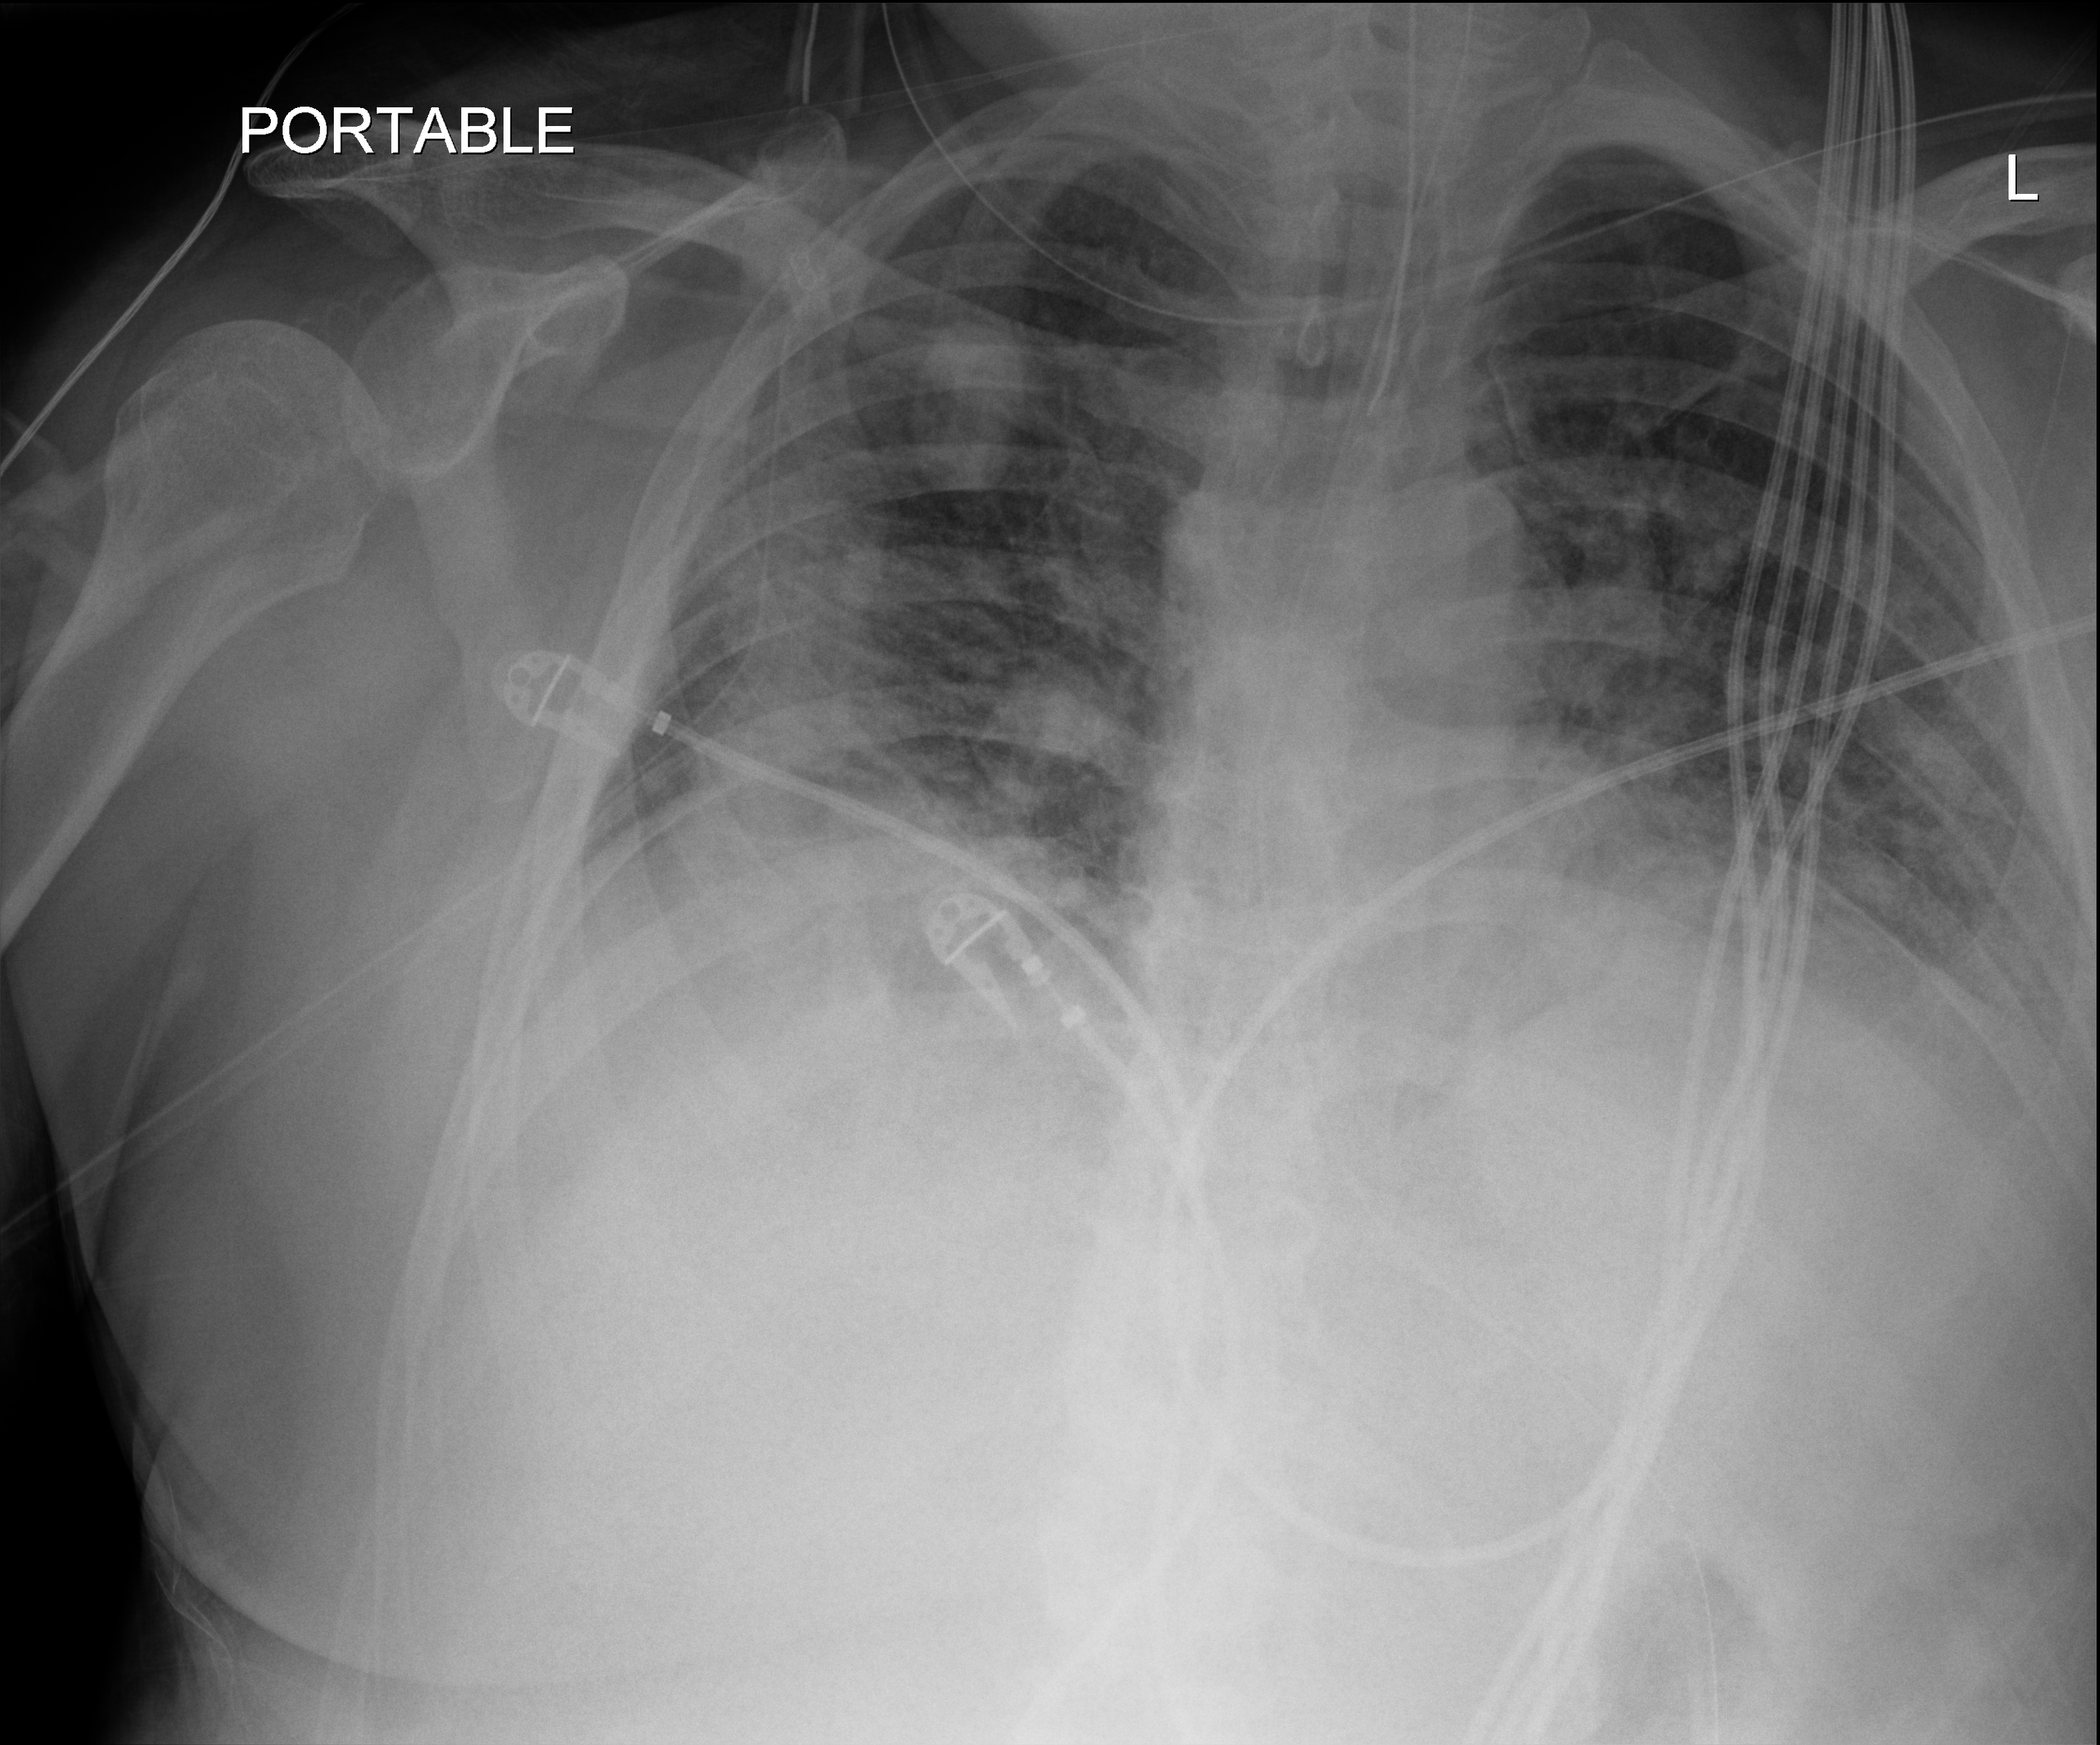
Bedside chest radiograph (digital radiography). Patient hospitalised with COVID-19; female, aged 60–74 years.
From the hospital-stay record, not from the radiograph (when in the stay this image was taken is not recorded): diabetes (admission record): no.